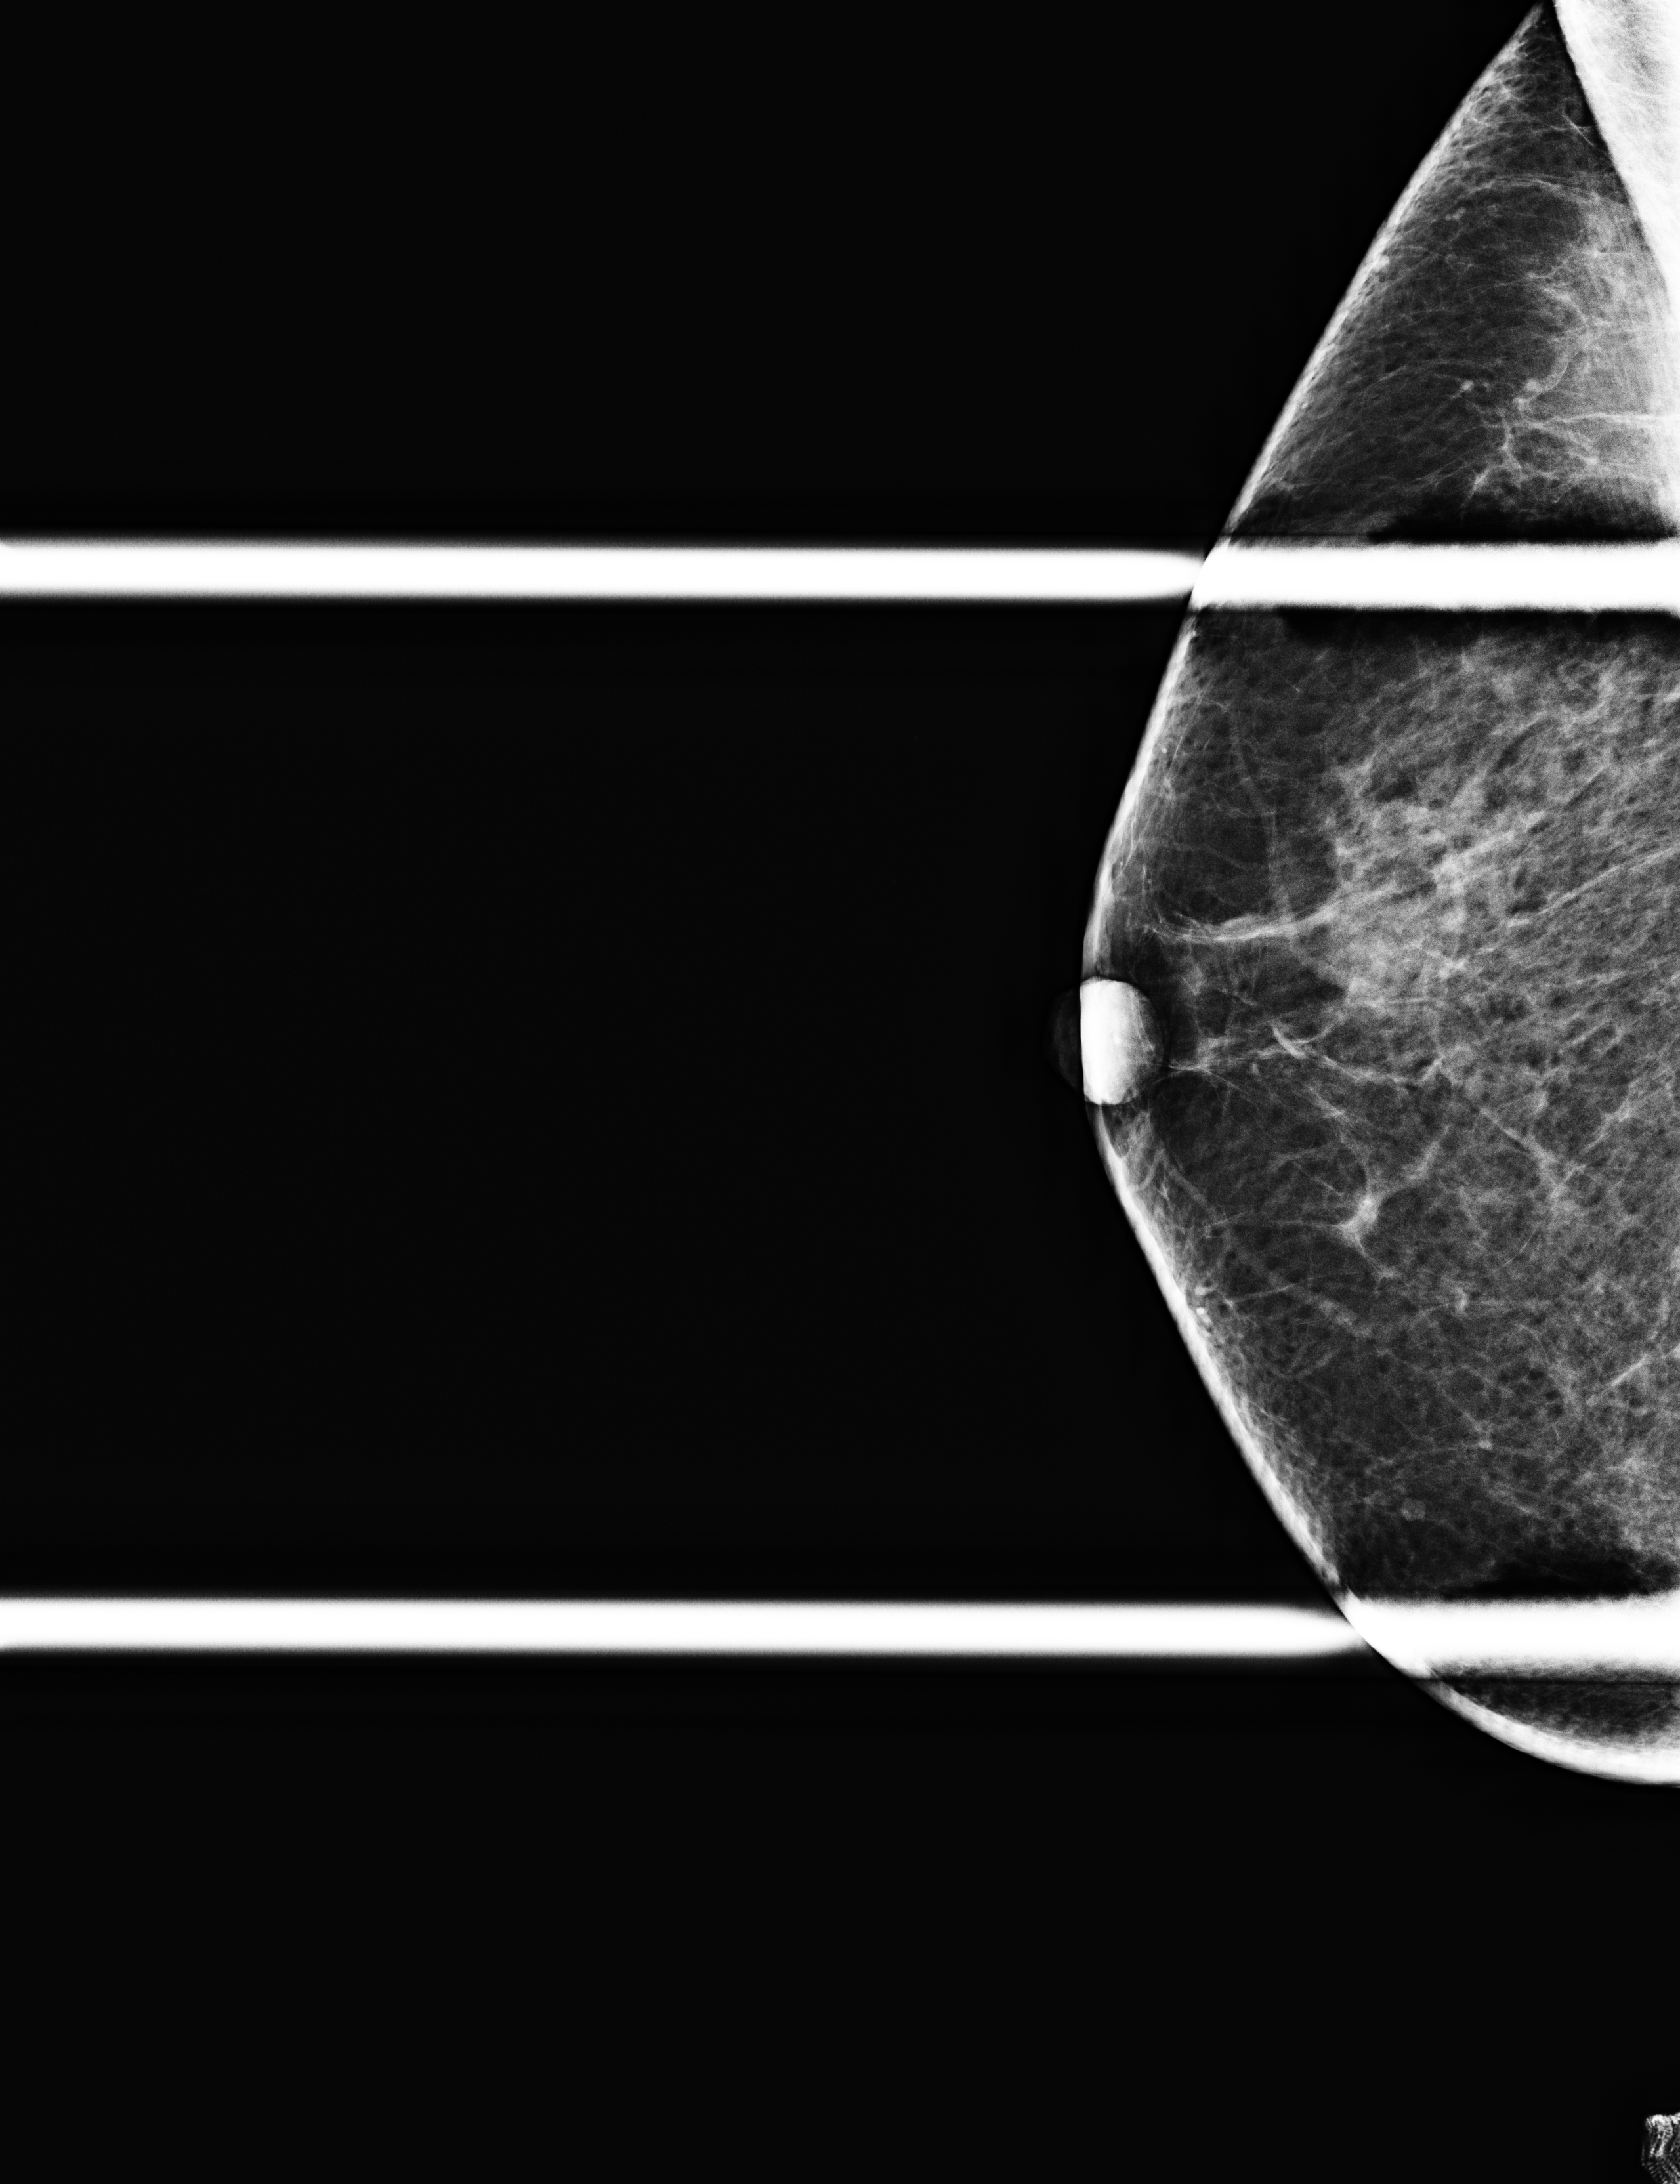
Full-field digital mammogram (FFDM); right breast; CC view (spot compression); additional work-up view; compressed breast thickness 49 mm; system: Selenia Dimensions. Patient: female, 61 years.
- breast density at the screening exam (both breasts): heterogeneously dense (BI-RADS density category c)
- final BI-RADS category for the screening round (tomosynthesis exam, both breasts): category 2
- recall: recalled for additional imaging after this screen